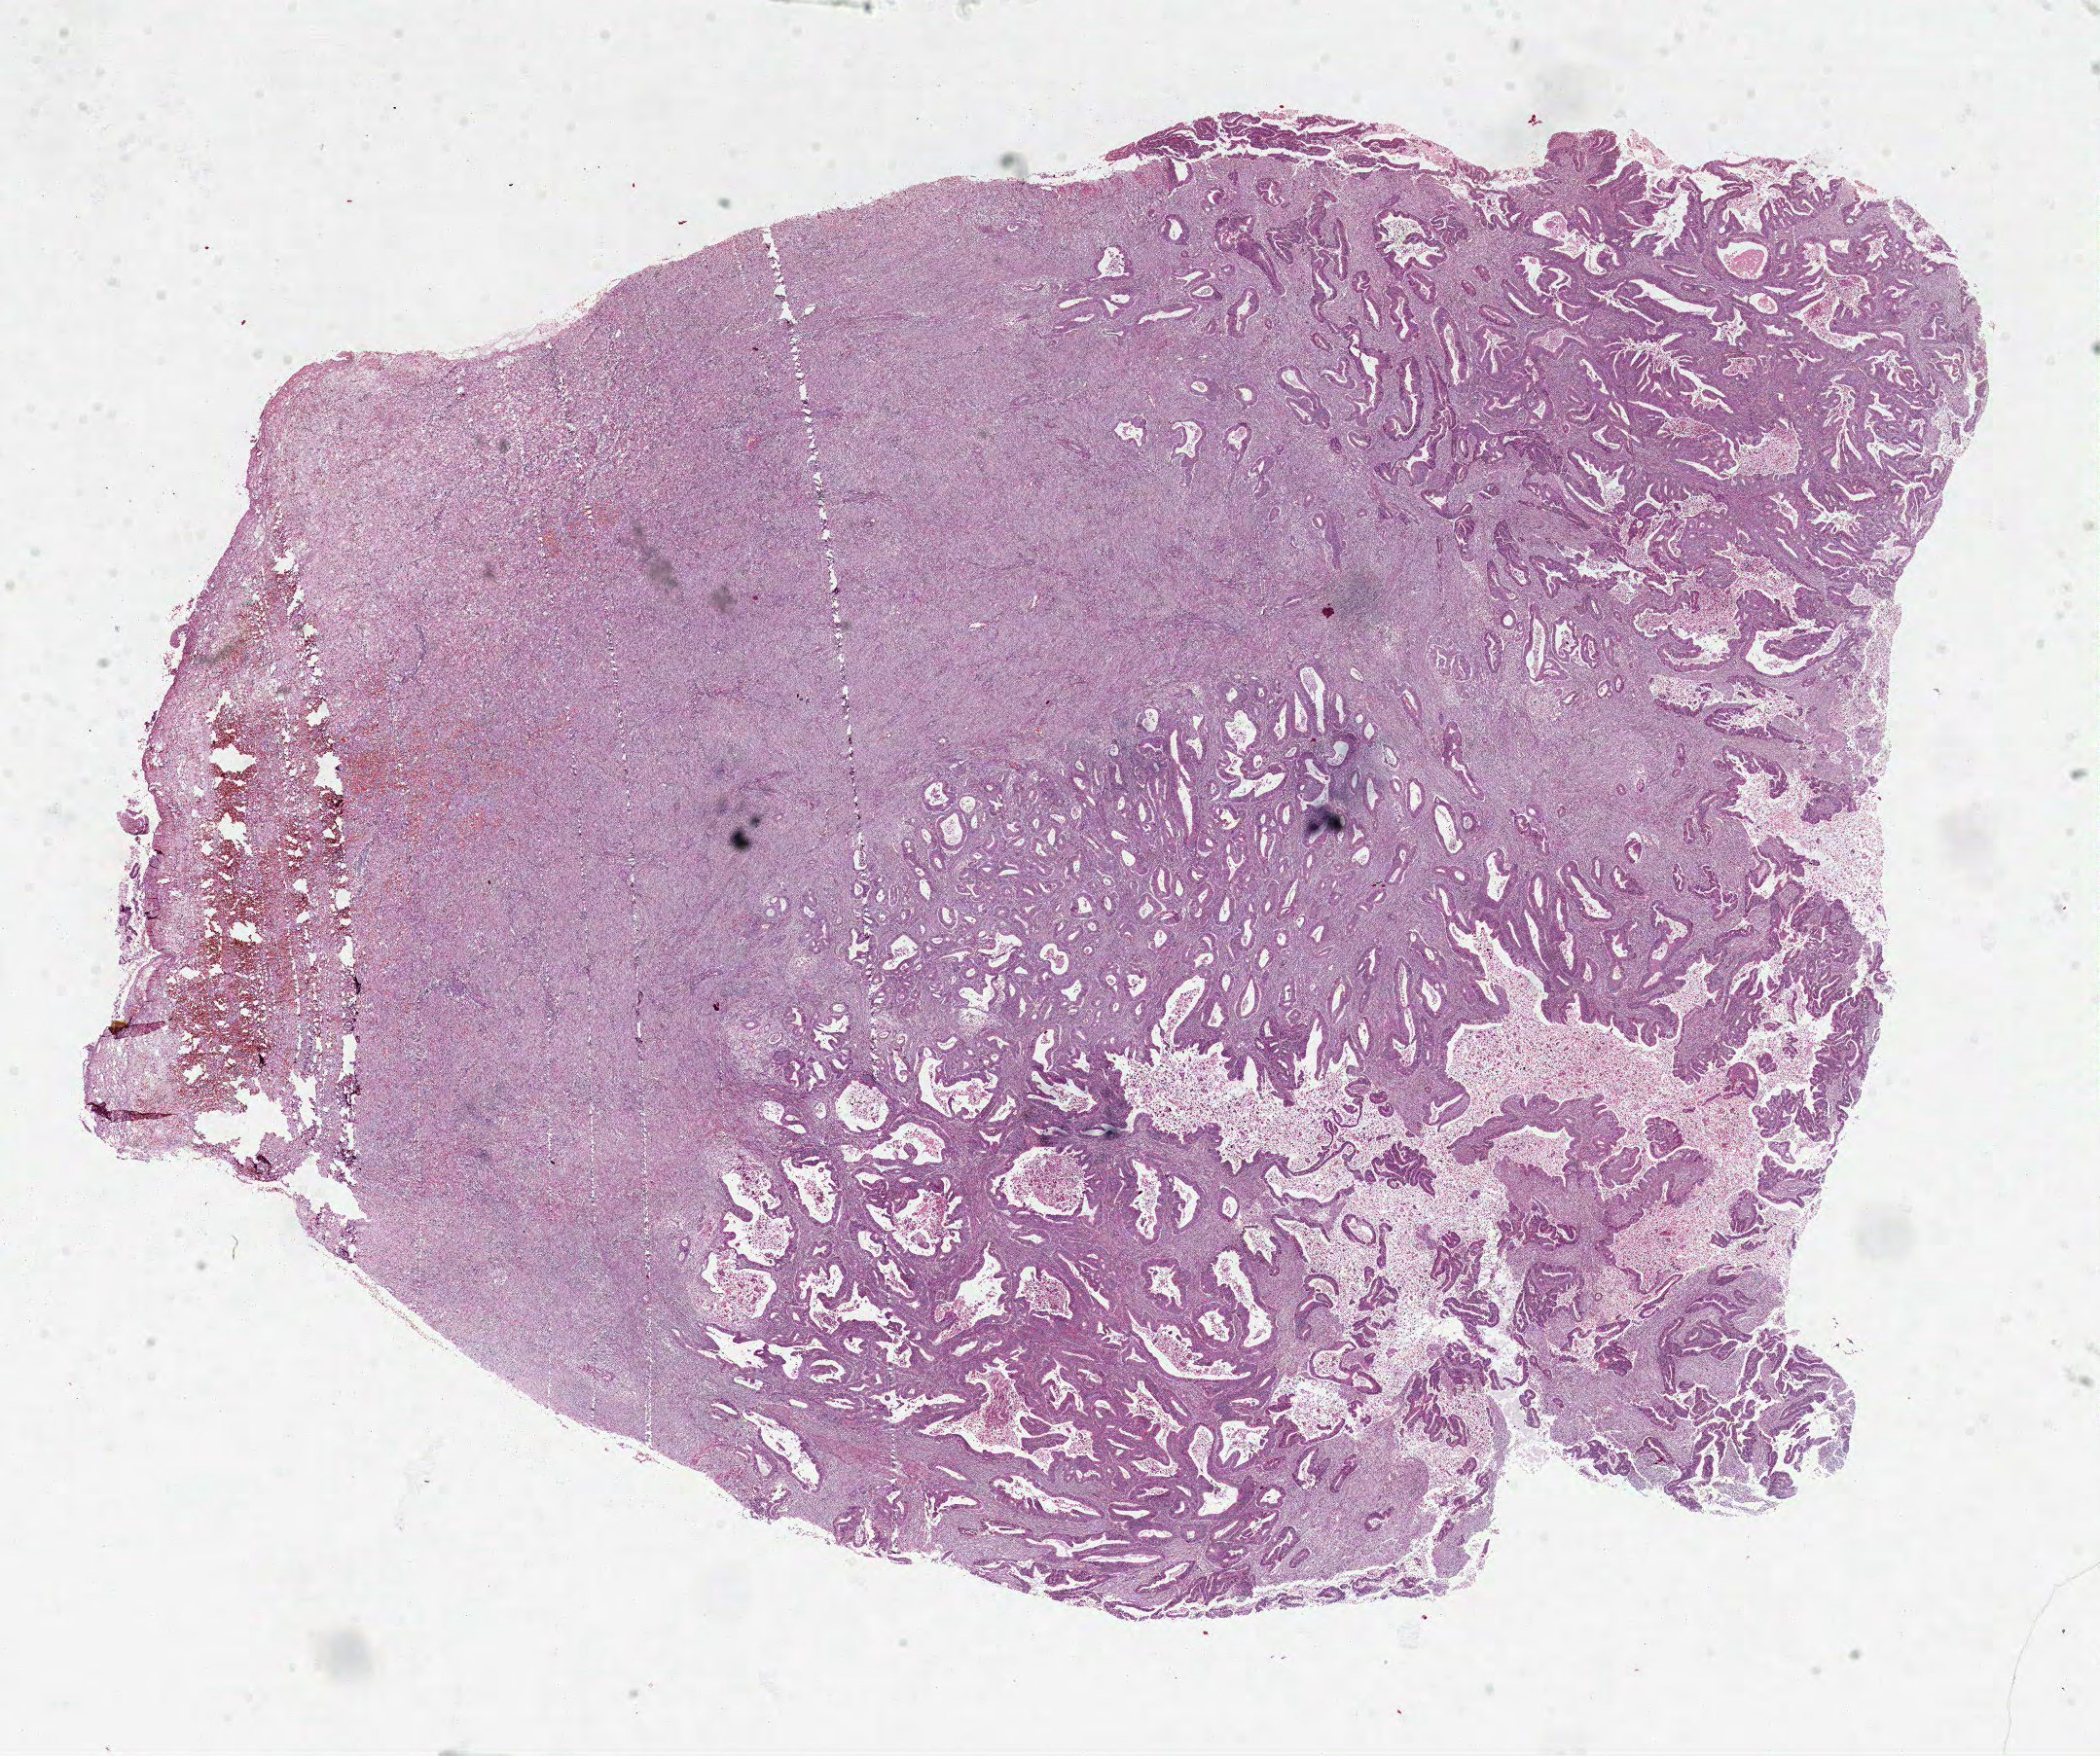
Digitized Hematoxylin and eosin (H&E) stained tissue section (whole slide) — low-resolution overview of the scanned area, about 17.4 x 14.6 mm (slide scanned at 40x), formalin-fixed paraffin-embedded (FFPE) diagnostic section, sample: primary tumour, colon. Female patient; age at initial diagnosis 42 years.
AJCC pathologic stage: IIA. Diagnosis: Adenocarcinoma, NOS.